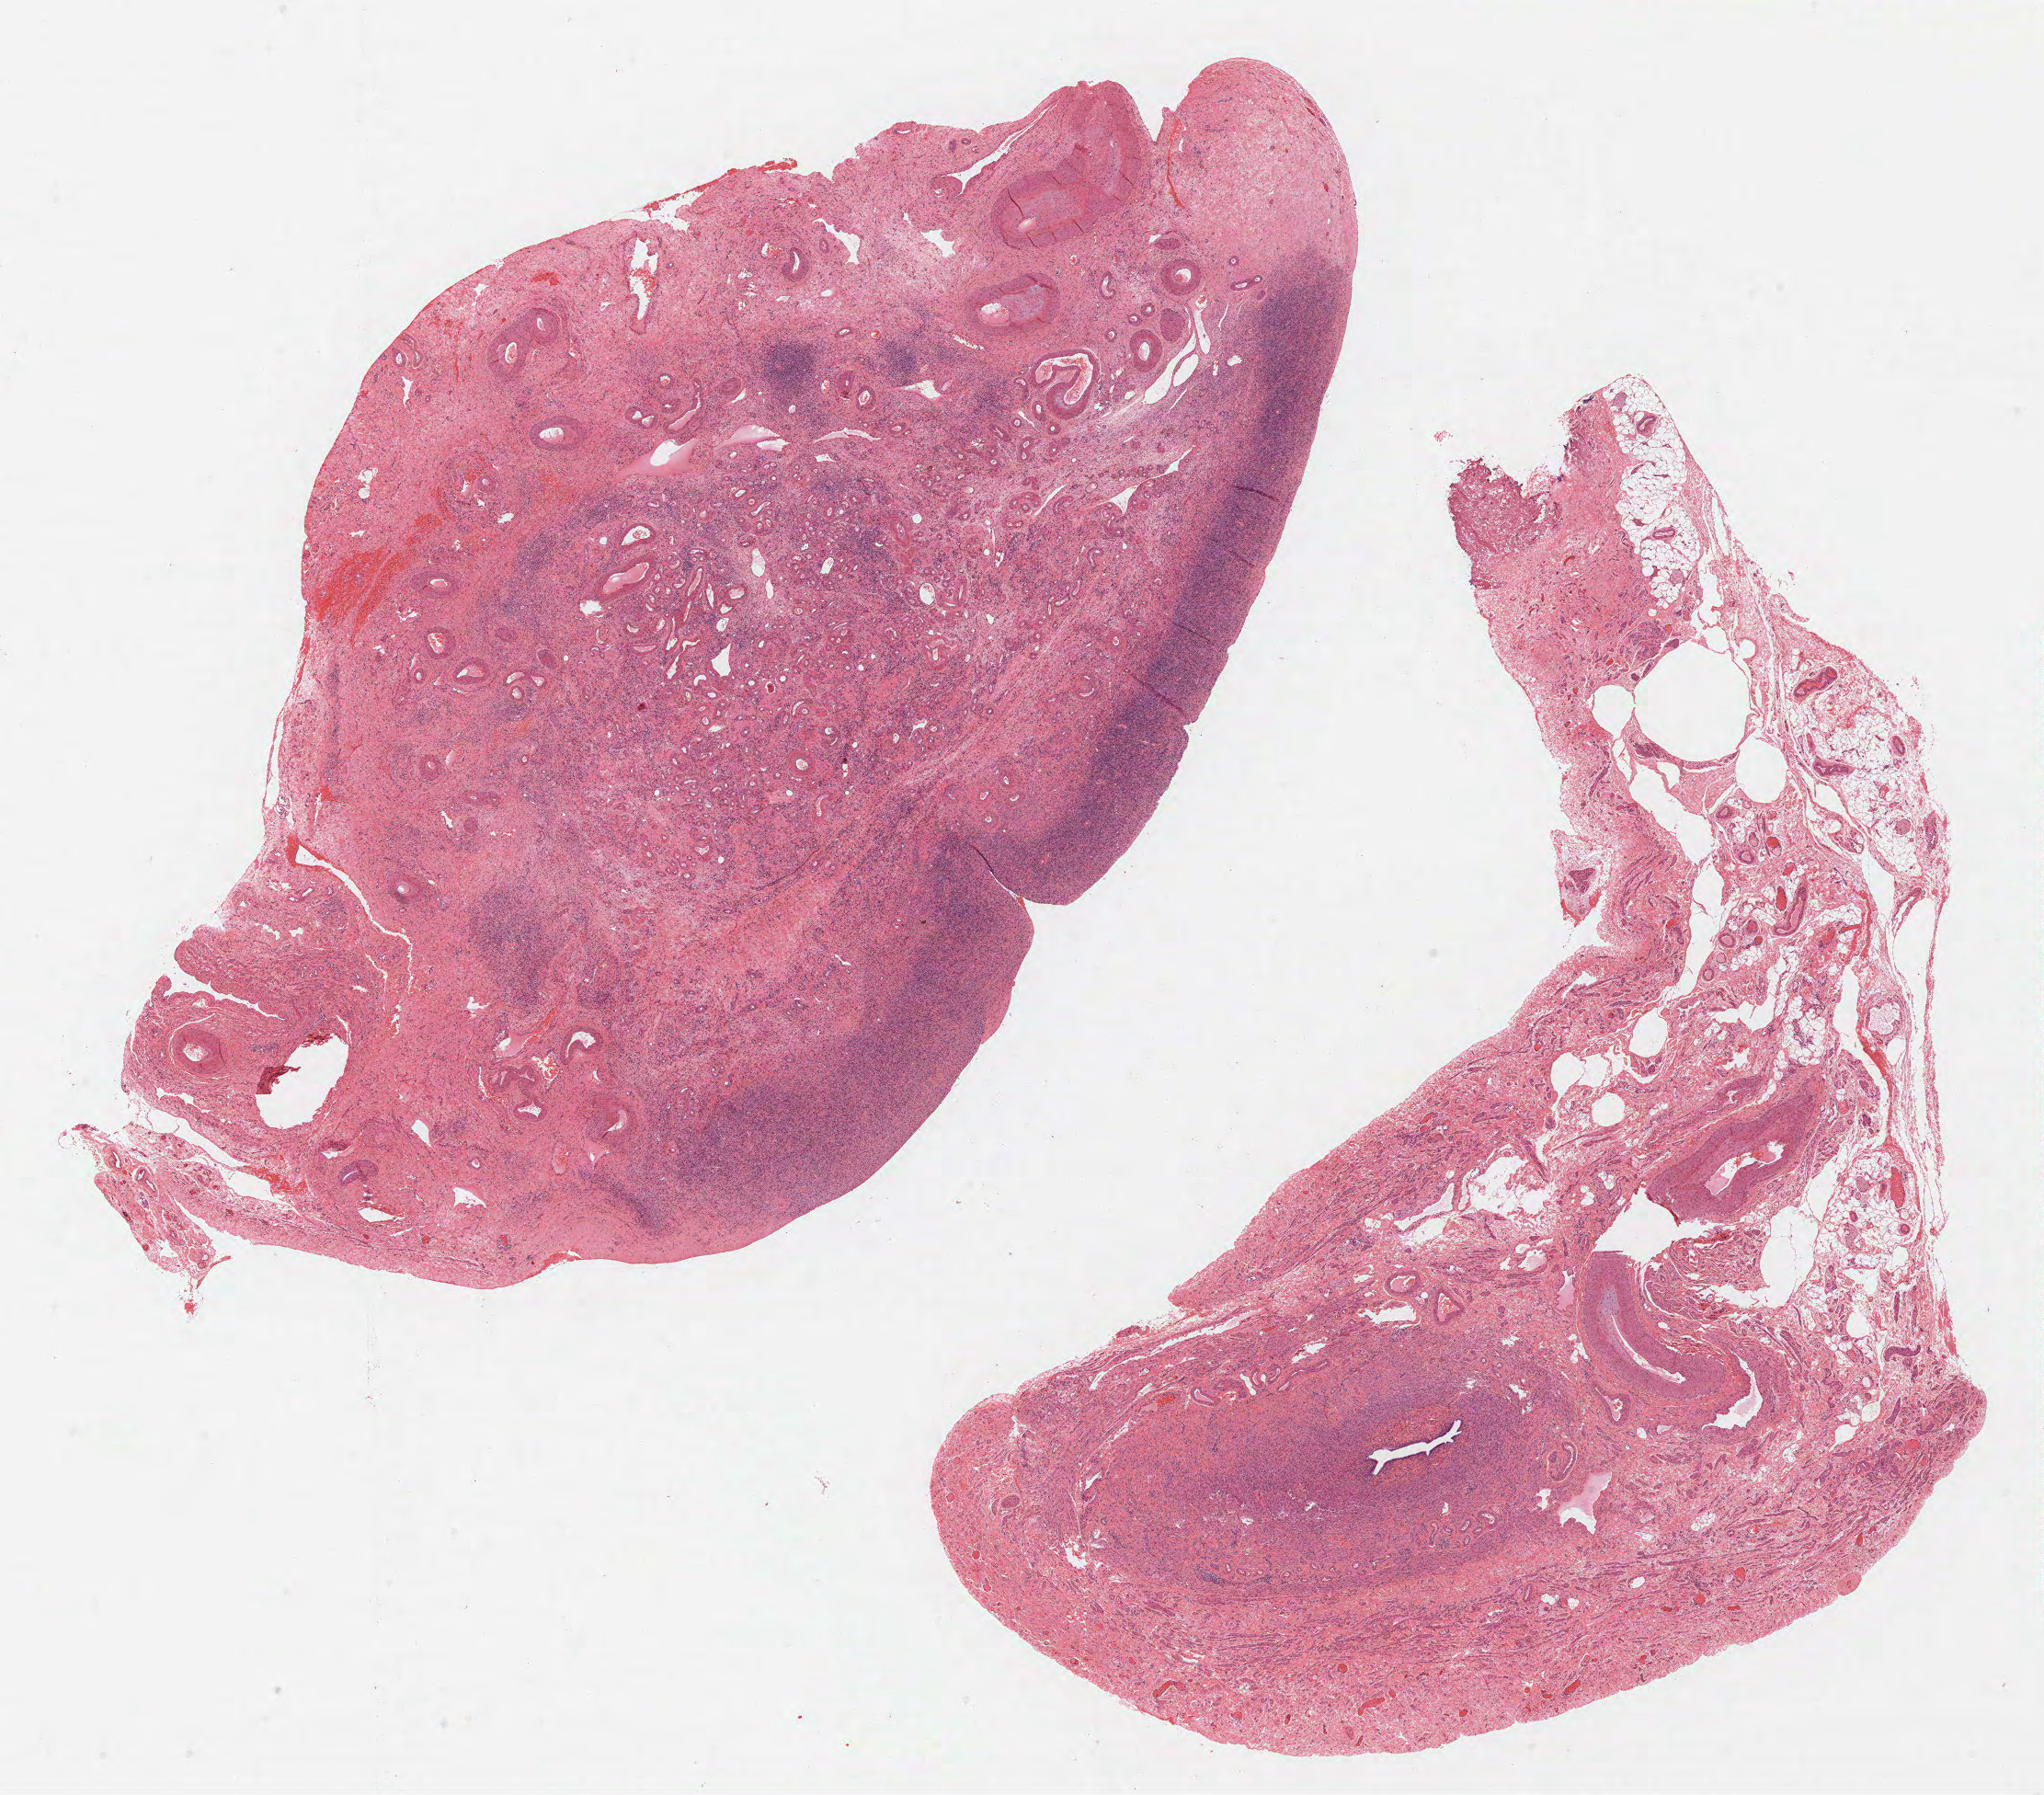
Hematoxylin and eosin (H&E) stained whole-slide image, whole scanned area (about 17.9 x 15.7 mm, slide scanned at 40x) shown as a low-resolution overview. Formalin-fixed paraffin-embedded (FFPE) diagnostic section. Sample: primary tumour, uterus. Female, age 56 years at initial diagnosis. Histologic grade: G3 (poorly differentiated).
• FIGO stage: IB
• diagnosis: Endometrioid adenocarcinoma, NOS (endometrium)
• lymph nodes positive (case pathology): 0 of 18 examined